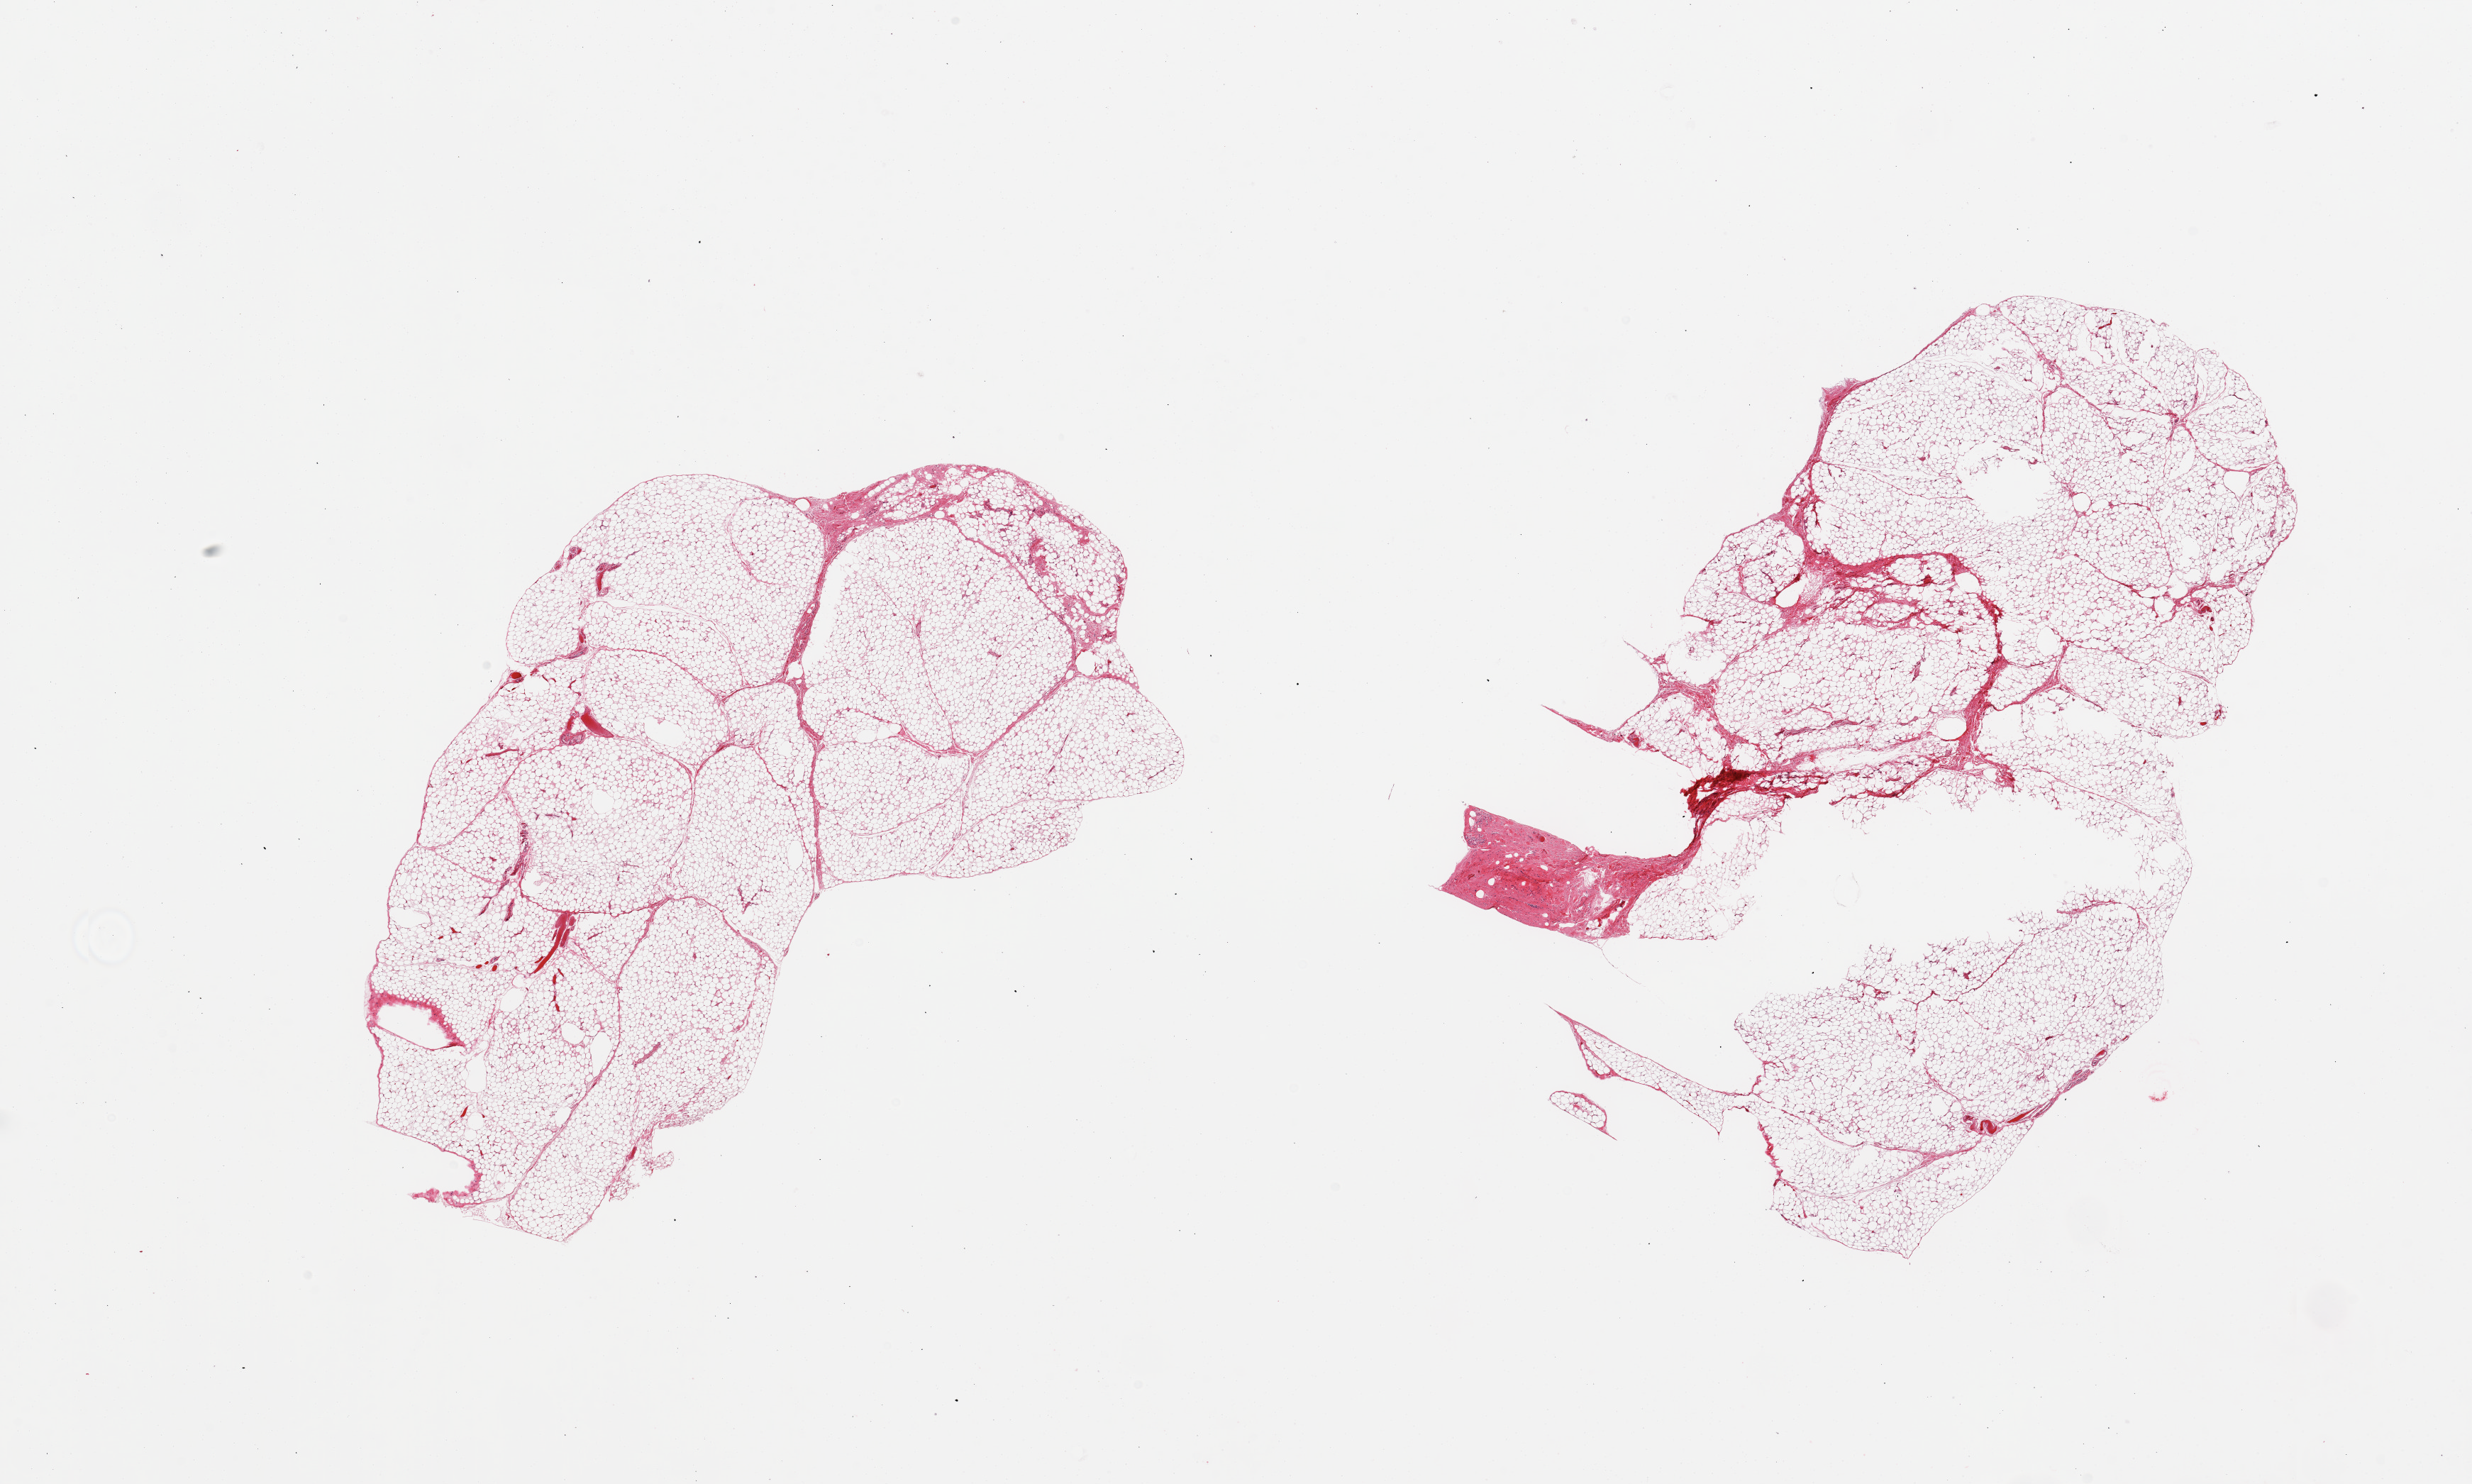
Hematoxylin and eosin (H&E) whole-slide image, whole scanned area (about 27.6 x 16.5 mm, slide scanned at 20x) shown as a low-resolution overview. PAXgene-fixed paraffin-embedded (PFPE) section. Section of omentum (target tissue). Tissue donor sample. Male donor.
Pathologist's review note for this sample: 2 pieces, ~10% interstitial fascia/mesothelial hyperplasia.